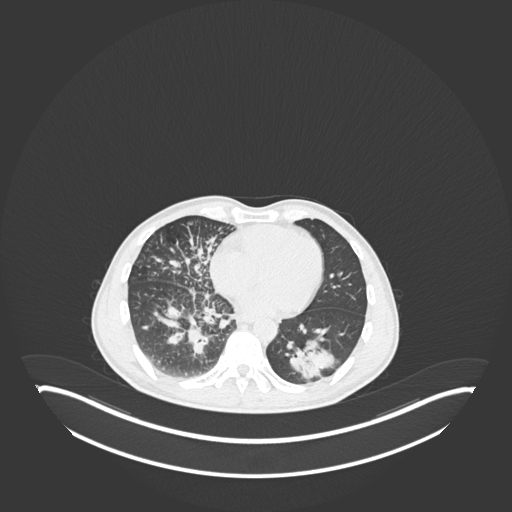
Chest CT, one axial slice. Slice 86 of 237 in the series (ordered by position). Reconstruction kernel B30f. Lung window (W 1500 / L -600 HU). 1 mm slice thickness. 512 × 512 image matrix, field of view 500 × 500 mm. Patient: male, 49 years. Case-level facts recorded for this patient, not image findings: clinical TNM (as recorded): T2b N1 M0.
Outlined on this slice (bounding box drawn by a radiologist):
- lung tumour (recorded histology: adenocarcinoma): bounding box (x1, y1, x2, y2) in pixels: (280, 332, 342, 383)